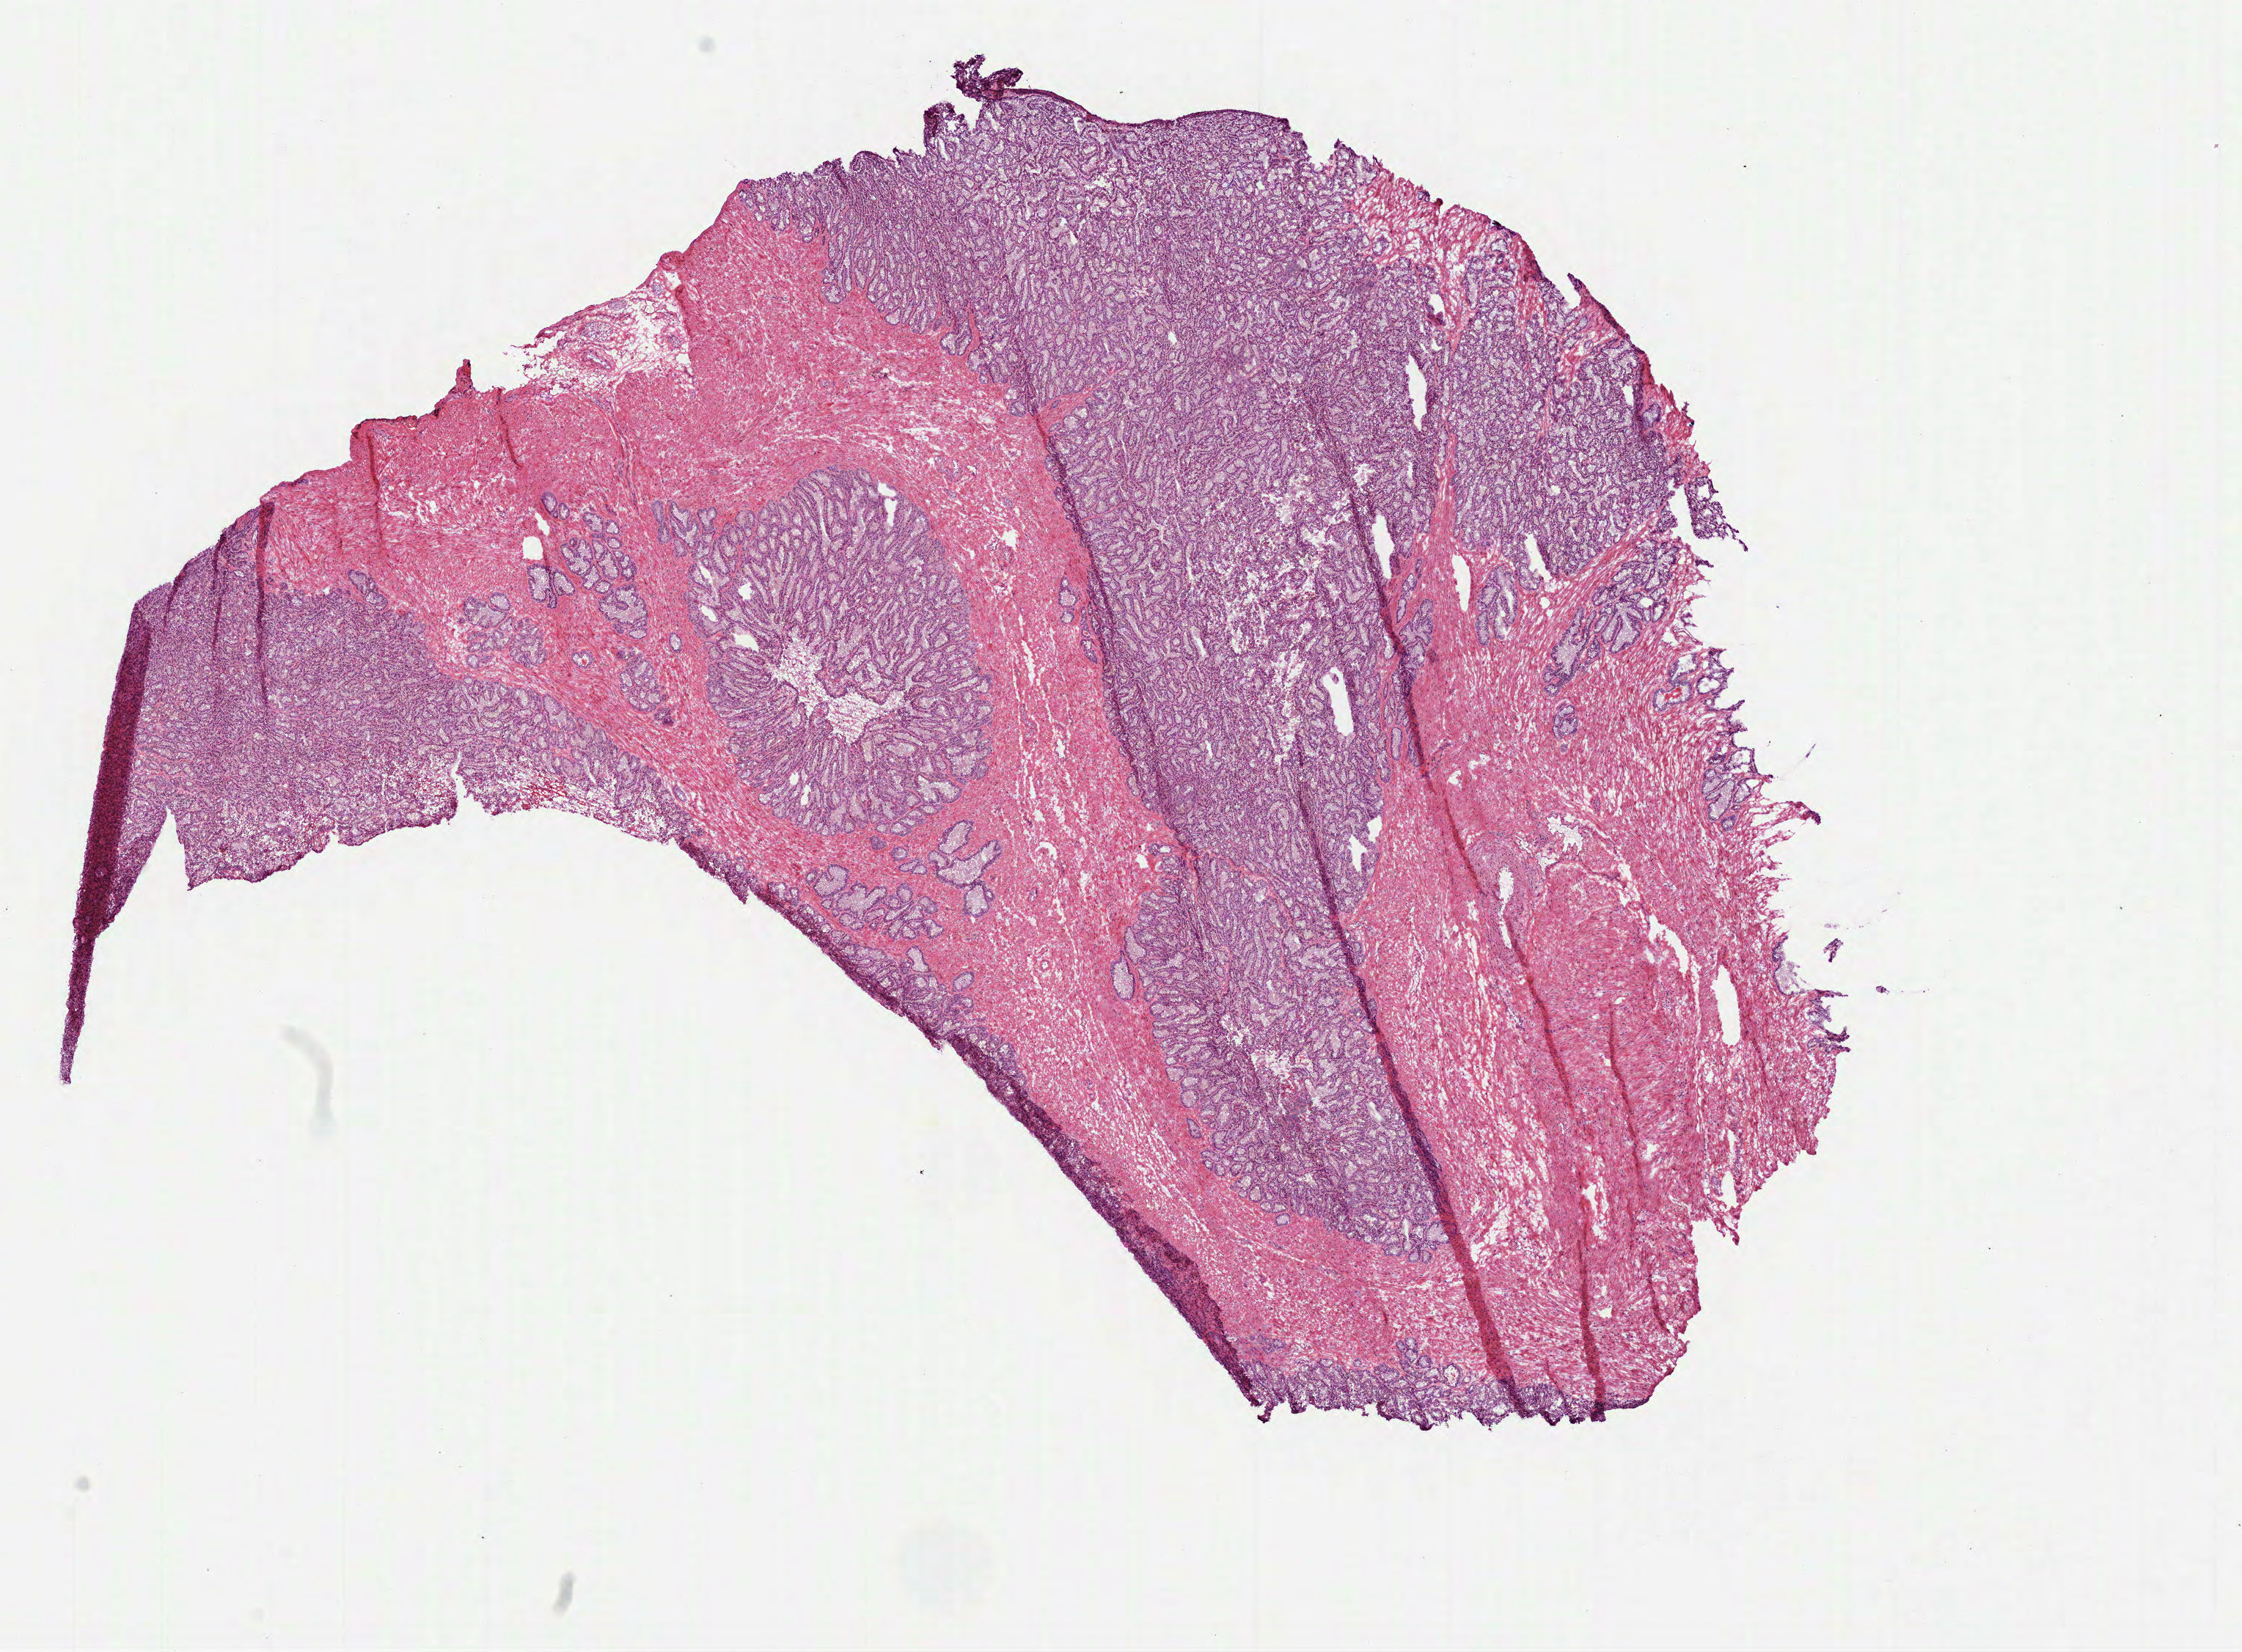
H&E-stained whole-slide image — whole scanned area (about 12.3 x 9.1 mm) shown as a low-resolution overview; frozen section; sample: solid tissue normal (non-tumour tissue), prostate. Male, age 52 years at initial diagnosis.
This section: solid tissue normal sample (biorepository sample class). Patient diagnosis: Acinar cell carcinoma (prostate gland).